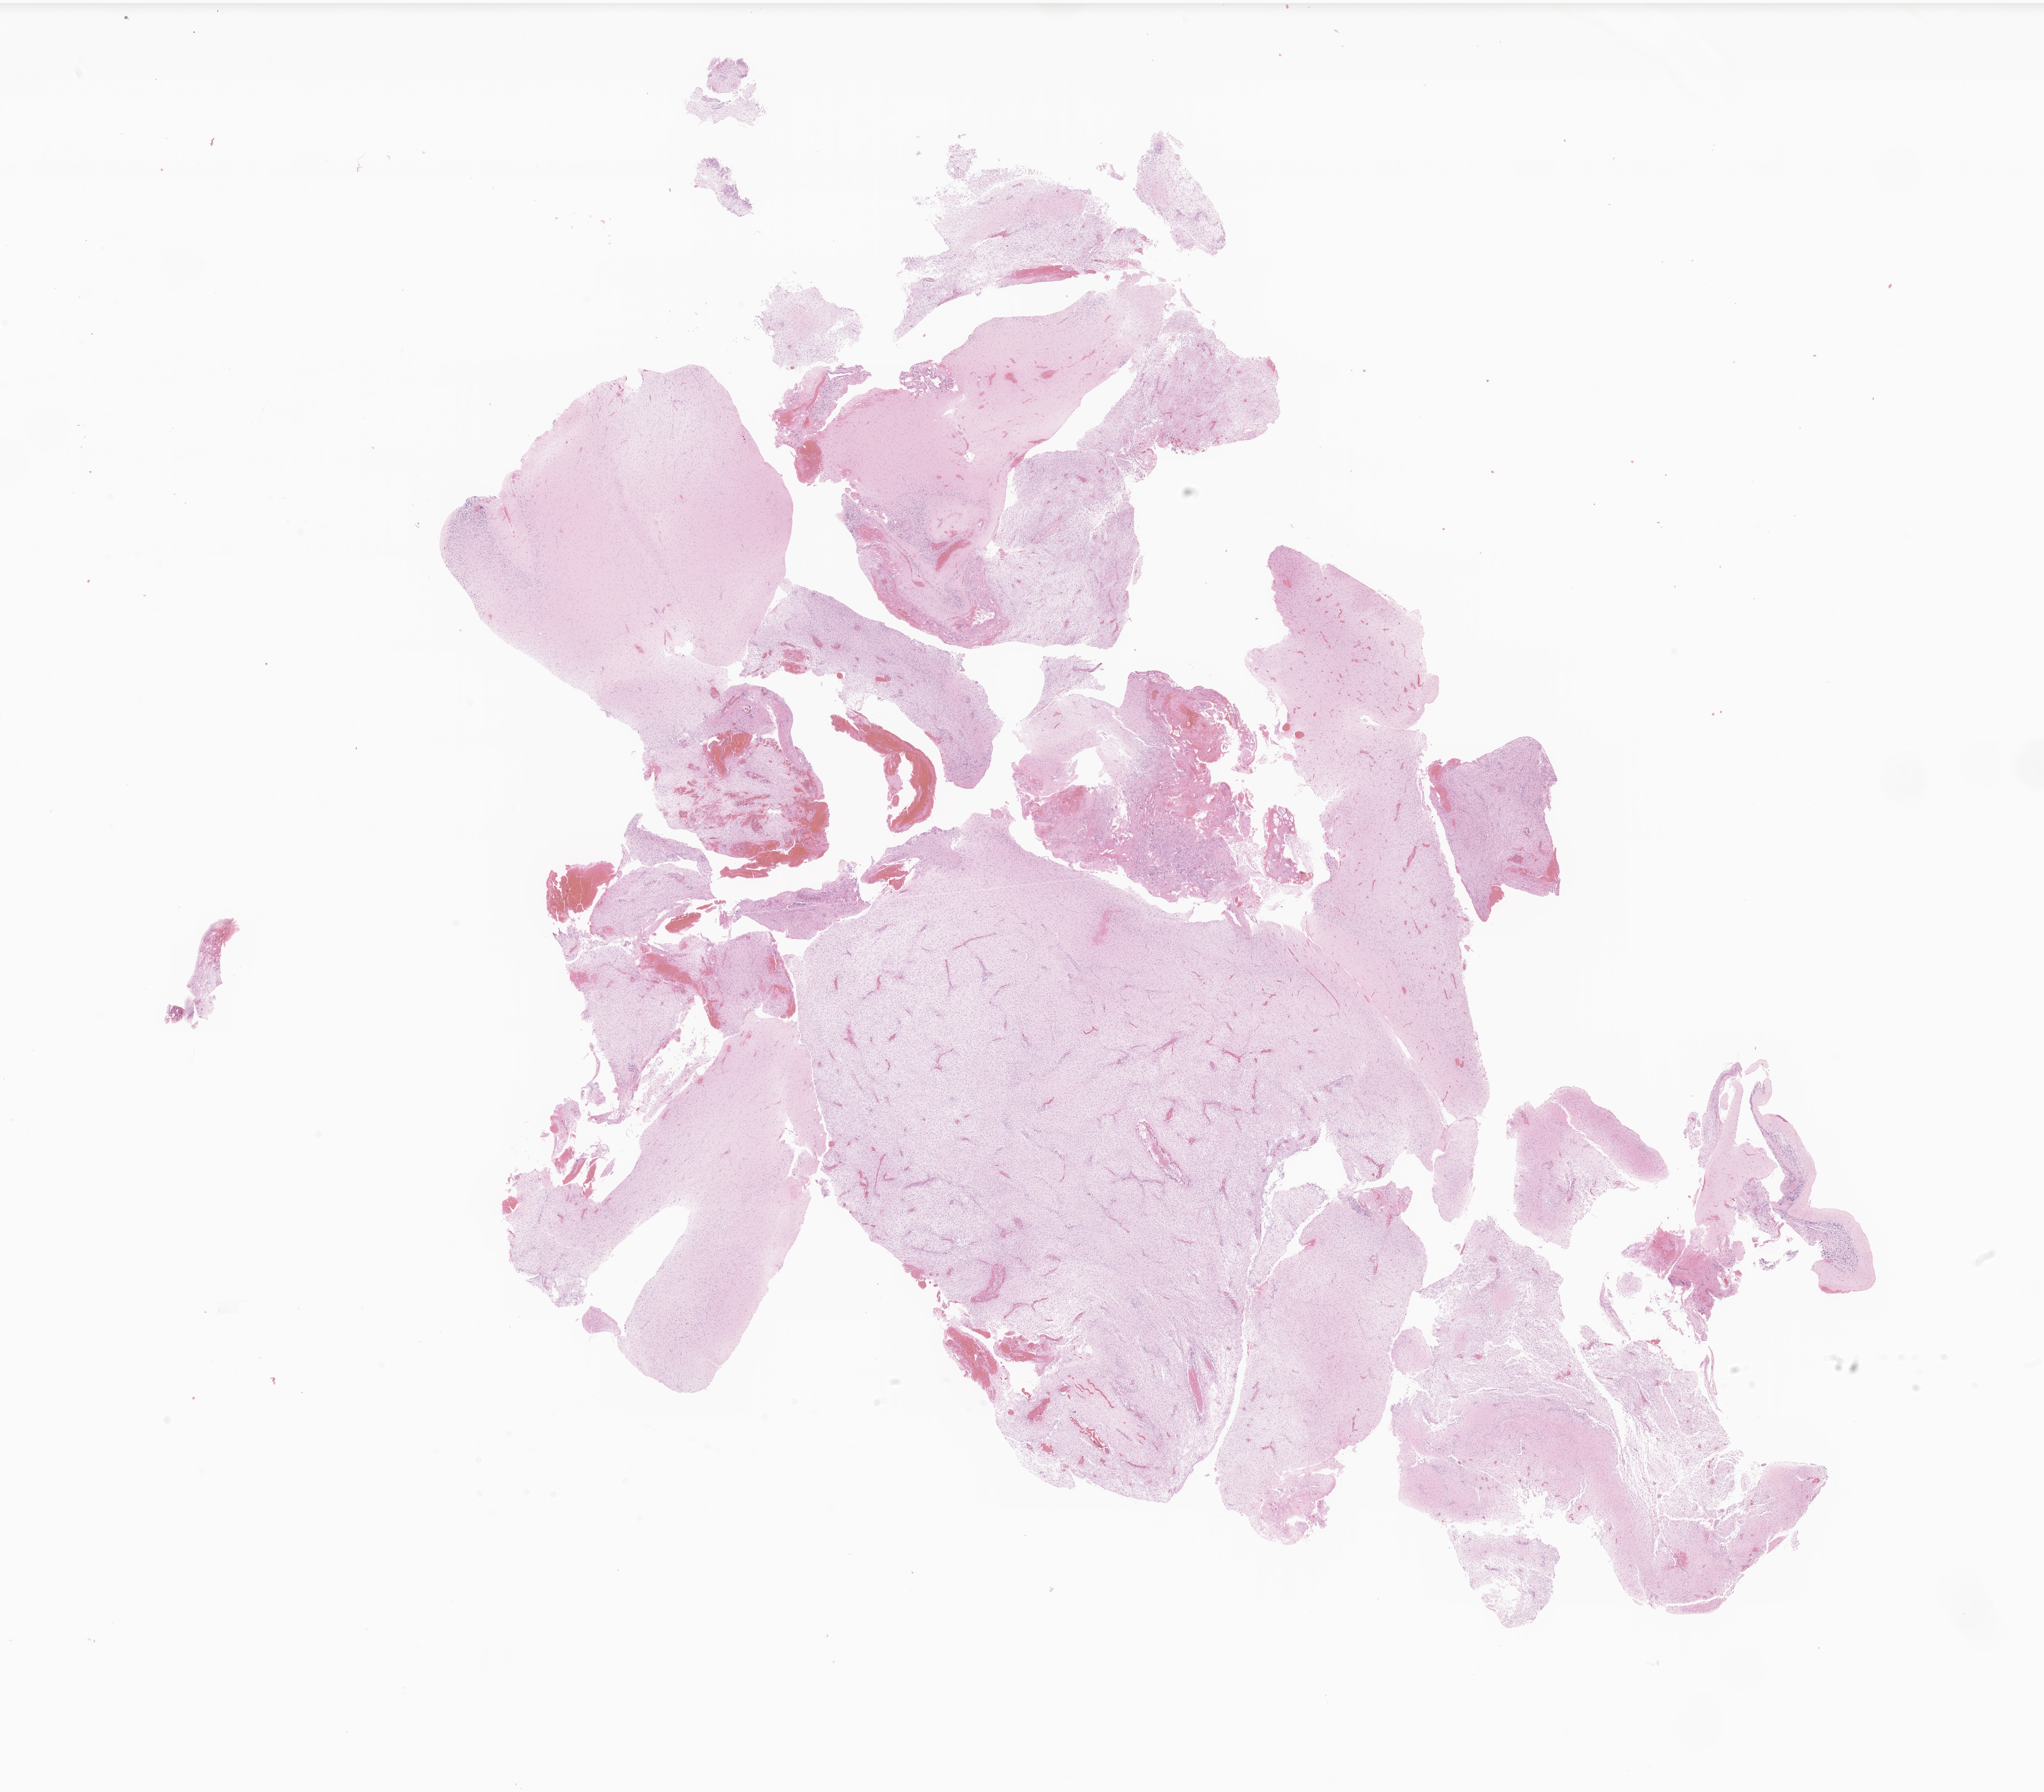
Haematoxylin and eosin whole-slide image of tumor tissue from the brain, low-resolution overview of the scanned area, about 22.9 x 20.1 mm, formalin-fixed paraffin-embedded section. Patient: female, age 34 months (2 years 10 months).
Diagnosis: Pilocytic astrocytoma.